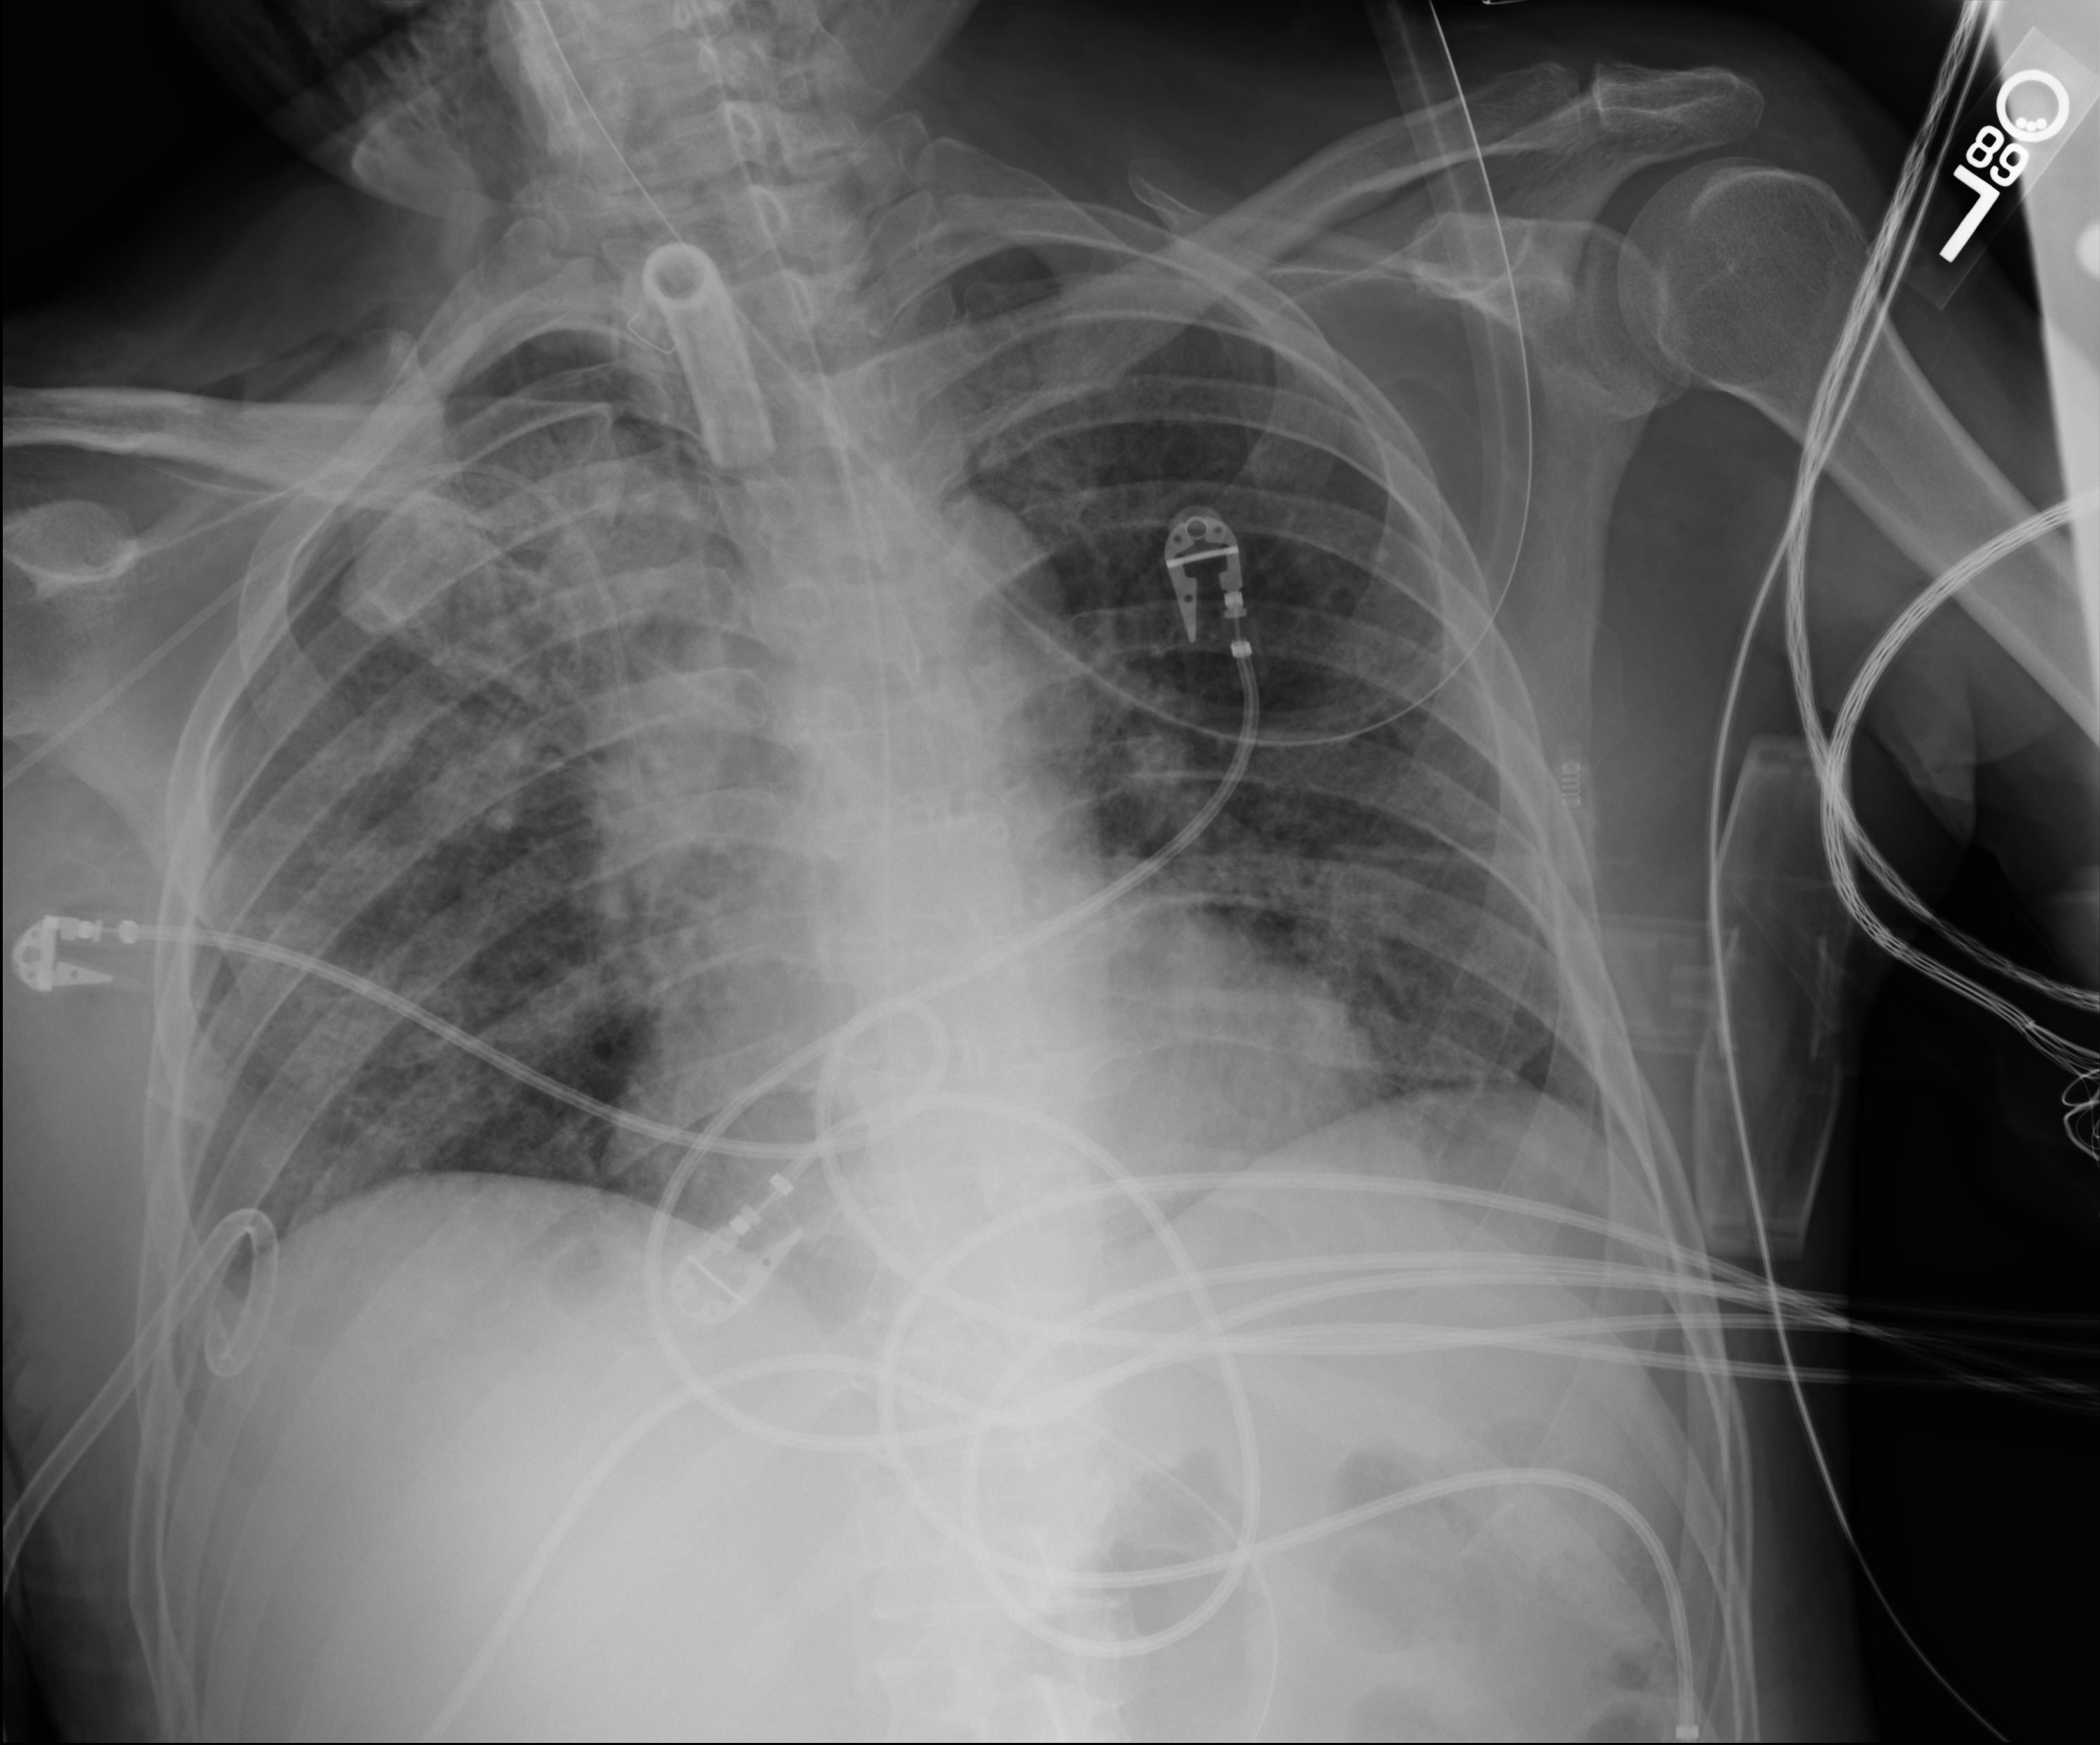
Chest X-ray (portable), anteroposterior (AP) projection. Male patient hospitalised with COVID-19, age 18–59 years.
Hospital-stay facts (about this admission, not read from this image; timing relative to this image not recorded): mechanically ventilated during this hospital stay: yes; COPD (admission record): no; admitted to intensive care during this hospital stay: yes.